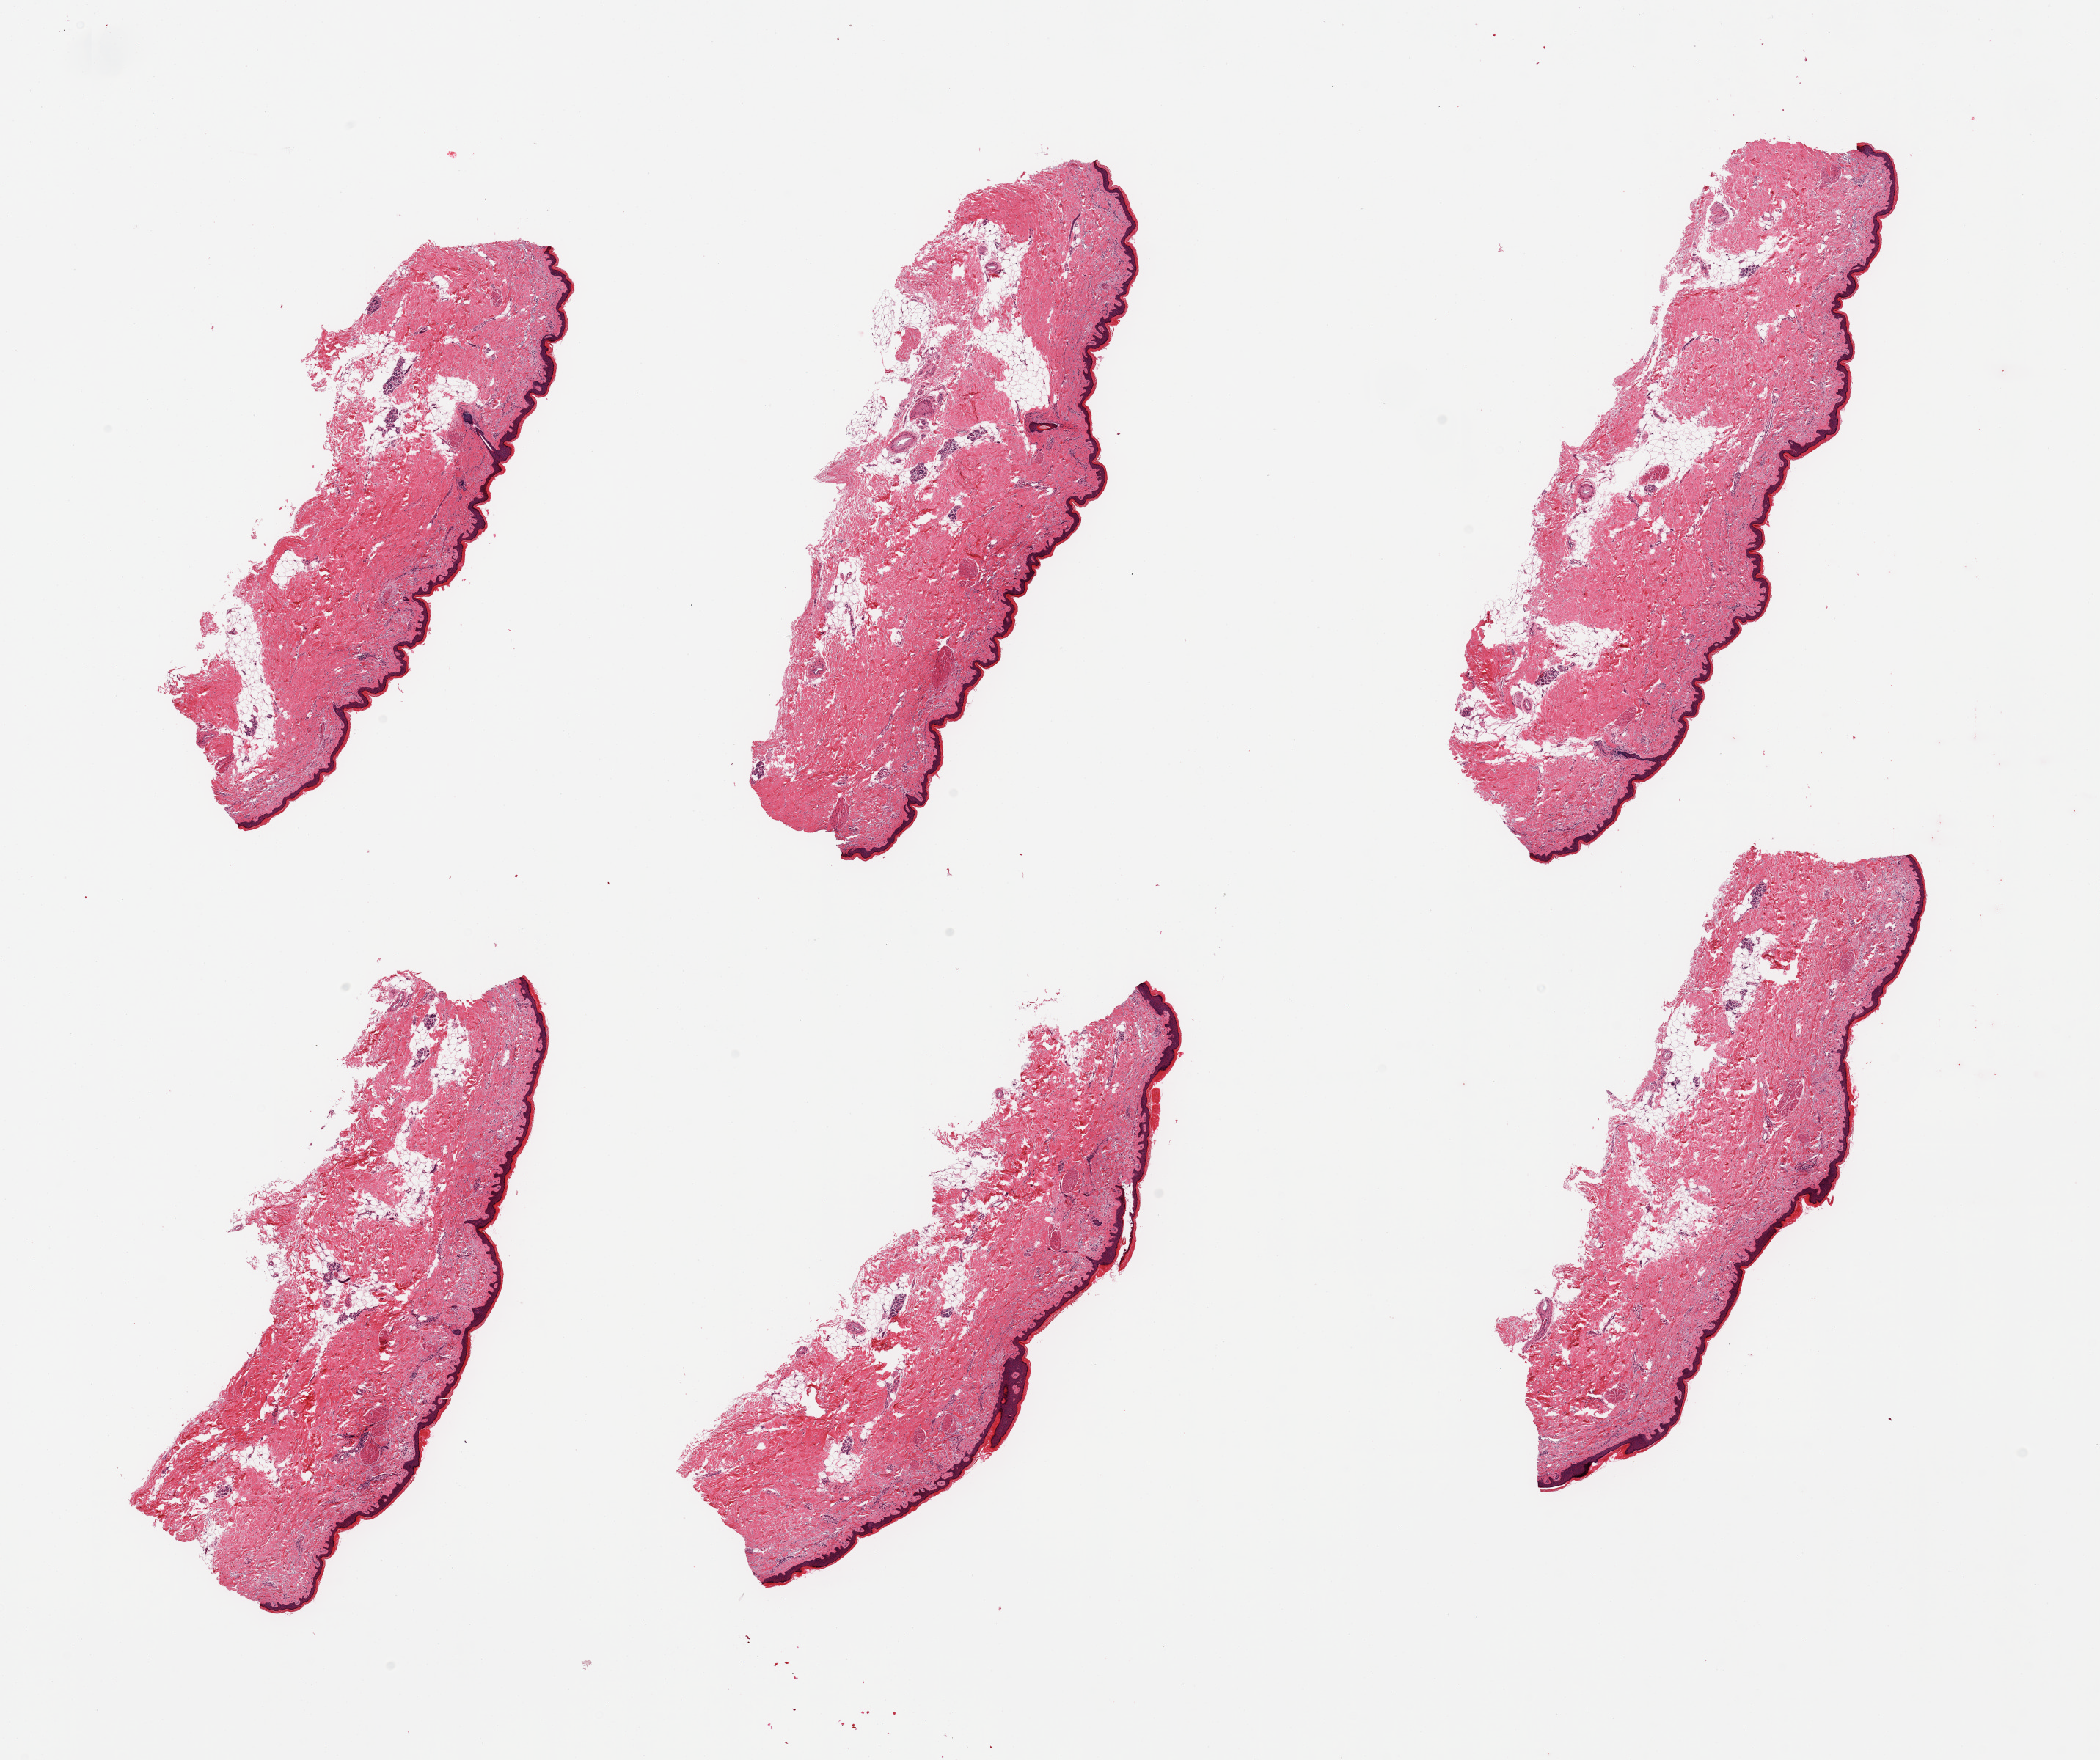
H&E whole-slide image, brightfield, a low-resolution overview of the entire scanned area, about 22.6 x 19.0 mm. PAXgene-fixed, paraffin-embedded tissue. Sampled site (target tissue): skin of lower leg. Donor tissue sample. Female donor.
Reviewer comment on this tissue sample: 6 pieces; 10% dermal fat; well trimmed.